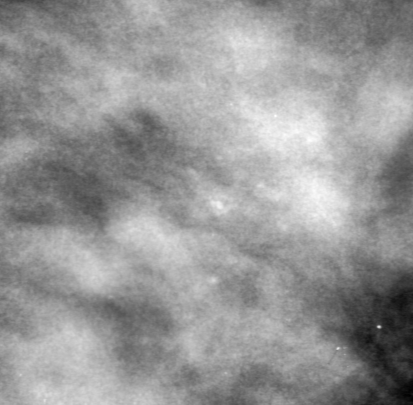
Region of interest cut from a scanned film mammogram (one marked finding); left breast; MLO view.
Finding: calcifications, morphology amorphous, distribution clustered; BI-RADS assessment category 0 (incomplete: needs additional imaging); subtlety rating 3 on a 1 (subtle) to 5 (obvious) scale; pathology (as recorded): benign.